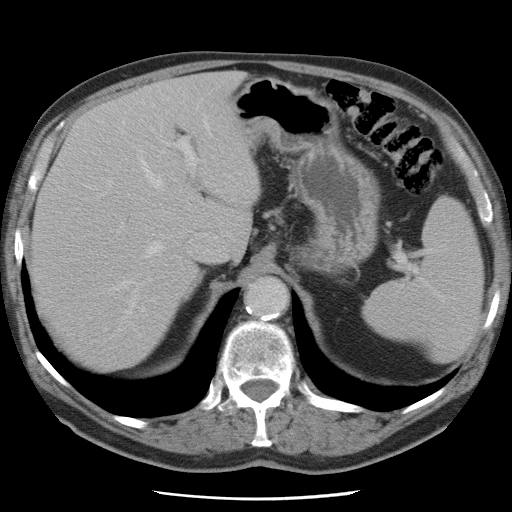
Contrast-enhanced abdominal CT, one axial slice; position 54 of 78 along the scan axis; 120 kVp; intravenous contrast given; soft-tissue window (W 400 / L 40 HU); 5 mm slice thickness; 512 × 512 image matrix. Male patient, age 75 years. Case-level facts recorded for this patient, not image findings: diagnosis: colorectal cancer liver metastases, imaged before liver resection; multiple liver metastases: yes; largest metastasis: 2.4 cm; disease in both lobes: yes.
Structures marked on this image (expert manual segmentation):
- hepatic veins: bounding box (x1, y1, x2, y2) in pixels: (98, 118, 208, 316)
- liver: (33, 74, 256, 366)
- planned liver remnant (the part of the liver to remain after resection): (33, 128, 196, 365)
- portal vein (with intrahepatic branches): (108, 138, 197, 234)